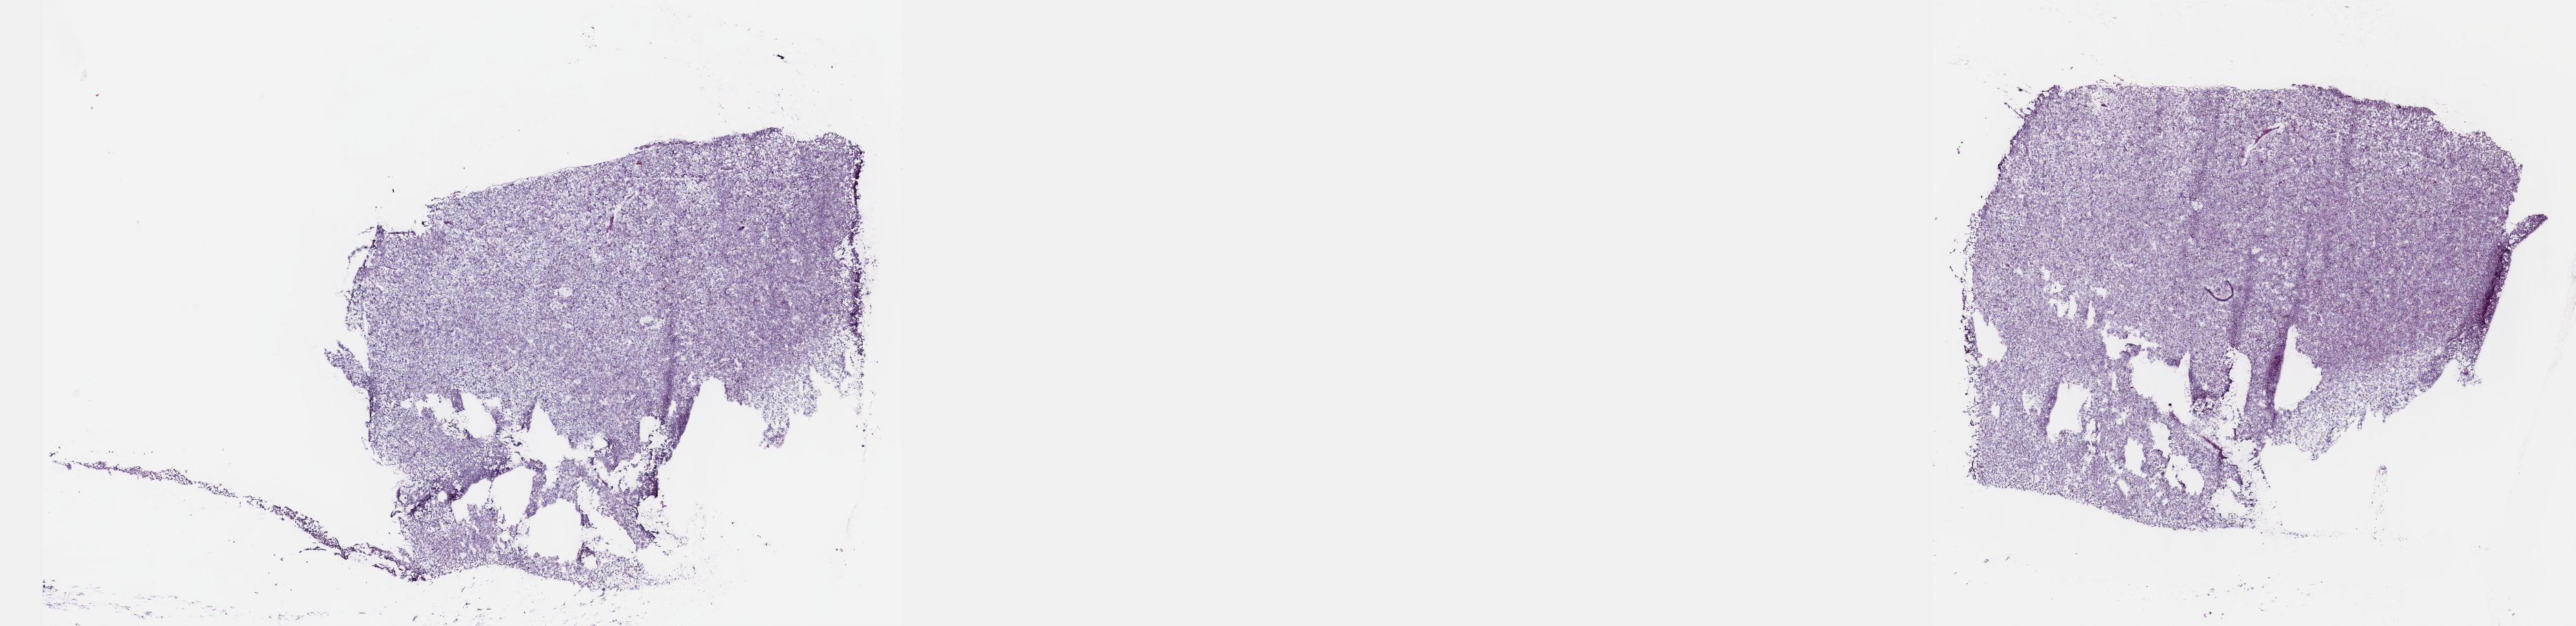
Whole-slide histology image, Hematoxylin and eosin (H&E) stained — whole scanned area (about 30.2 x 7.3 mm) shown as a low-resolution overview, frozen section from the top of the tissue portion, primary tumour sample from the brain. Male, age 34 years at initial diagnosis. Histologic grade: G2 (moderately differentiated). Composition of this section per pathologist review: tumour cells 50%, tumour nuclei 80%, normal cells 10%, stromal cells 40%, necrosis 0%. Inflammatory infiltration, as recorded: lymphocyte infiltration 0%, monocyte infiltration 0%, neutrophil infiltration 0%.
Diagnosis: Oligodendroglioma, NOS.